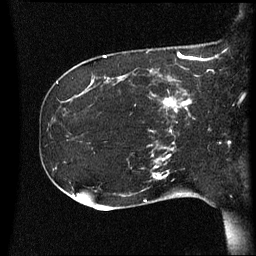
Breast MRI (dynamic contrast-enhanced), one sagittal slice. Slice 17 of 60 in the series (ordered by position). Dynamic contrast-enhanced series, image 2 of 3 at this slice position (ordered by acquisition). 1.5 T. TE 4.2 ms, TR 8.4 ms. 2.2 mm slice thickness. 256 × 256 image matrix, field of view 220 × 220 mm. Female patient, age 41 years. From the clinical record (not read from this slice): setting: breast cancer imaged before/during neoadjuvant chemotherapy; receptor status: HER2-positive.
Annotated regions visible in this slice (semi-automatically segmented with operator editing):
- analysis volume of interest (the breast-tissue region the enhancement analysis was run in; not a lesion): box from (x=122, y=80) to (x=197, y=125) px
- tumour enhancement mask (voxels above the 70 % enhancement threshold inside the analysis volume of interest): (x=162, y=92)–(x=193, y=117)